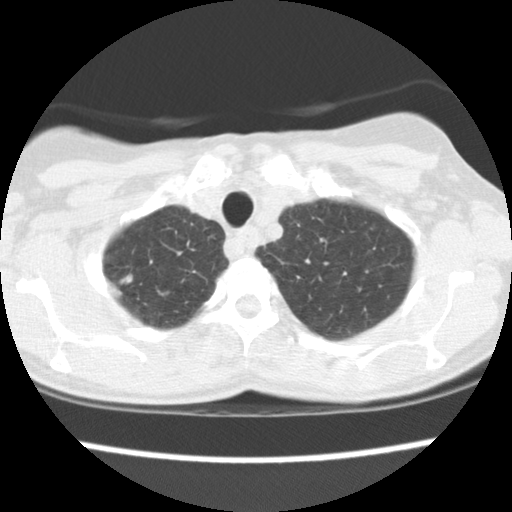
Low-dose screening chest CT, one axial slice. Slice 130 of 148 in the series (ordered by position). 120 kVp. Lung window (W 1500 / L -600 HU). 2.5 mm slice thickness. 512 × 512 image matrix.
Annotated regions visible in this slice (manually delineated by an expert):
- lesion 1 (tumor): bounding box (x1, y1, x2, y2) in pixels: (120, 274, 133, 284)